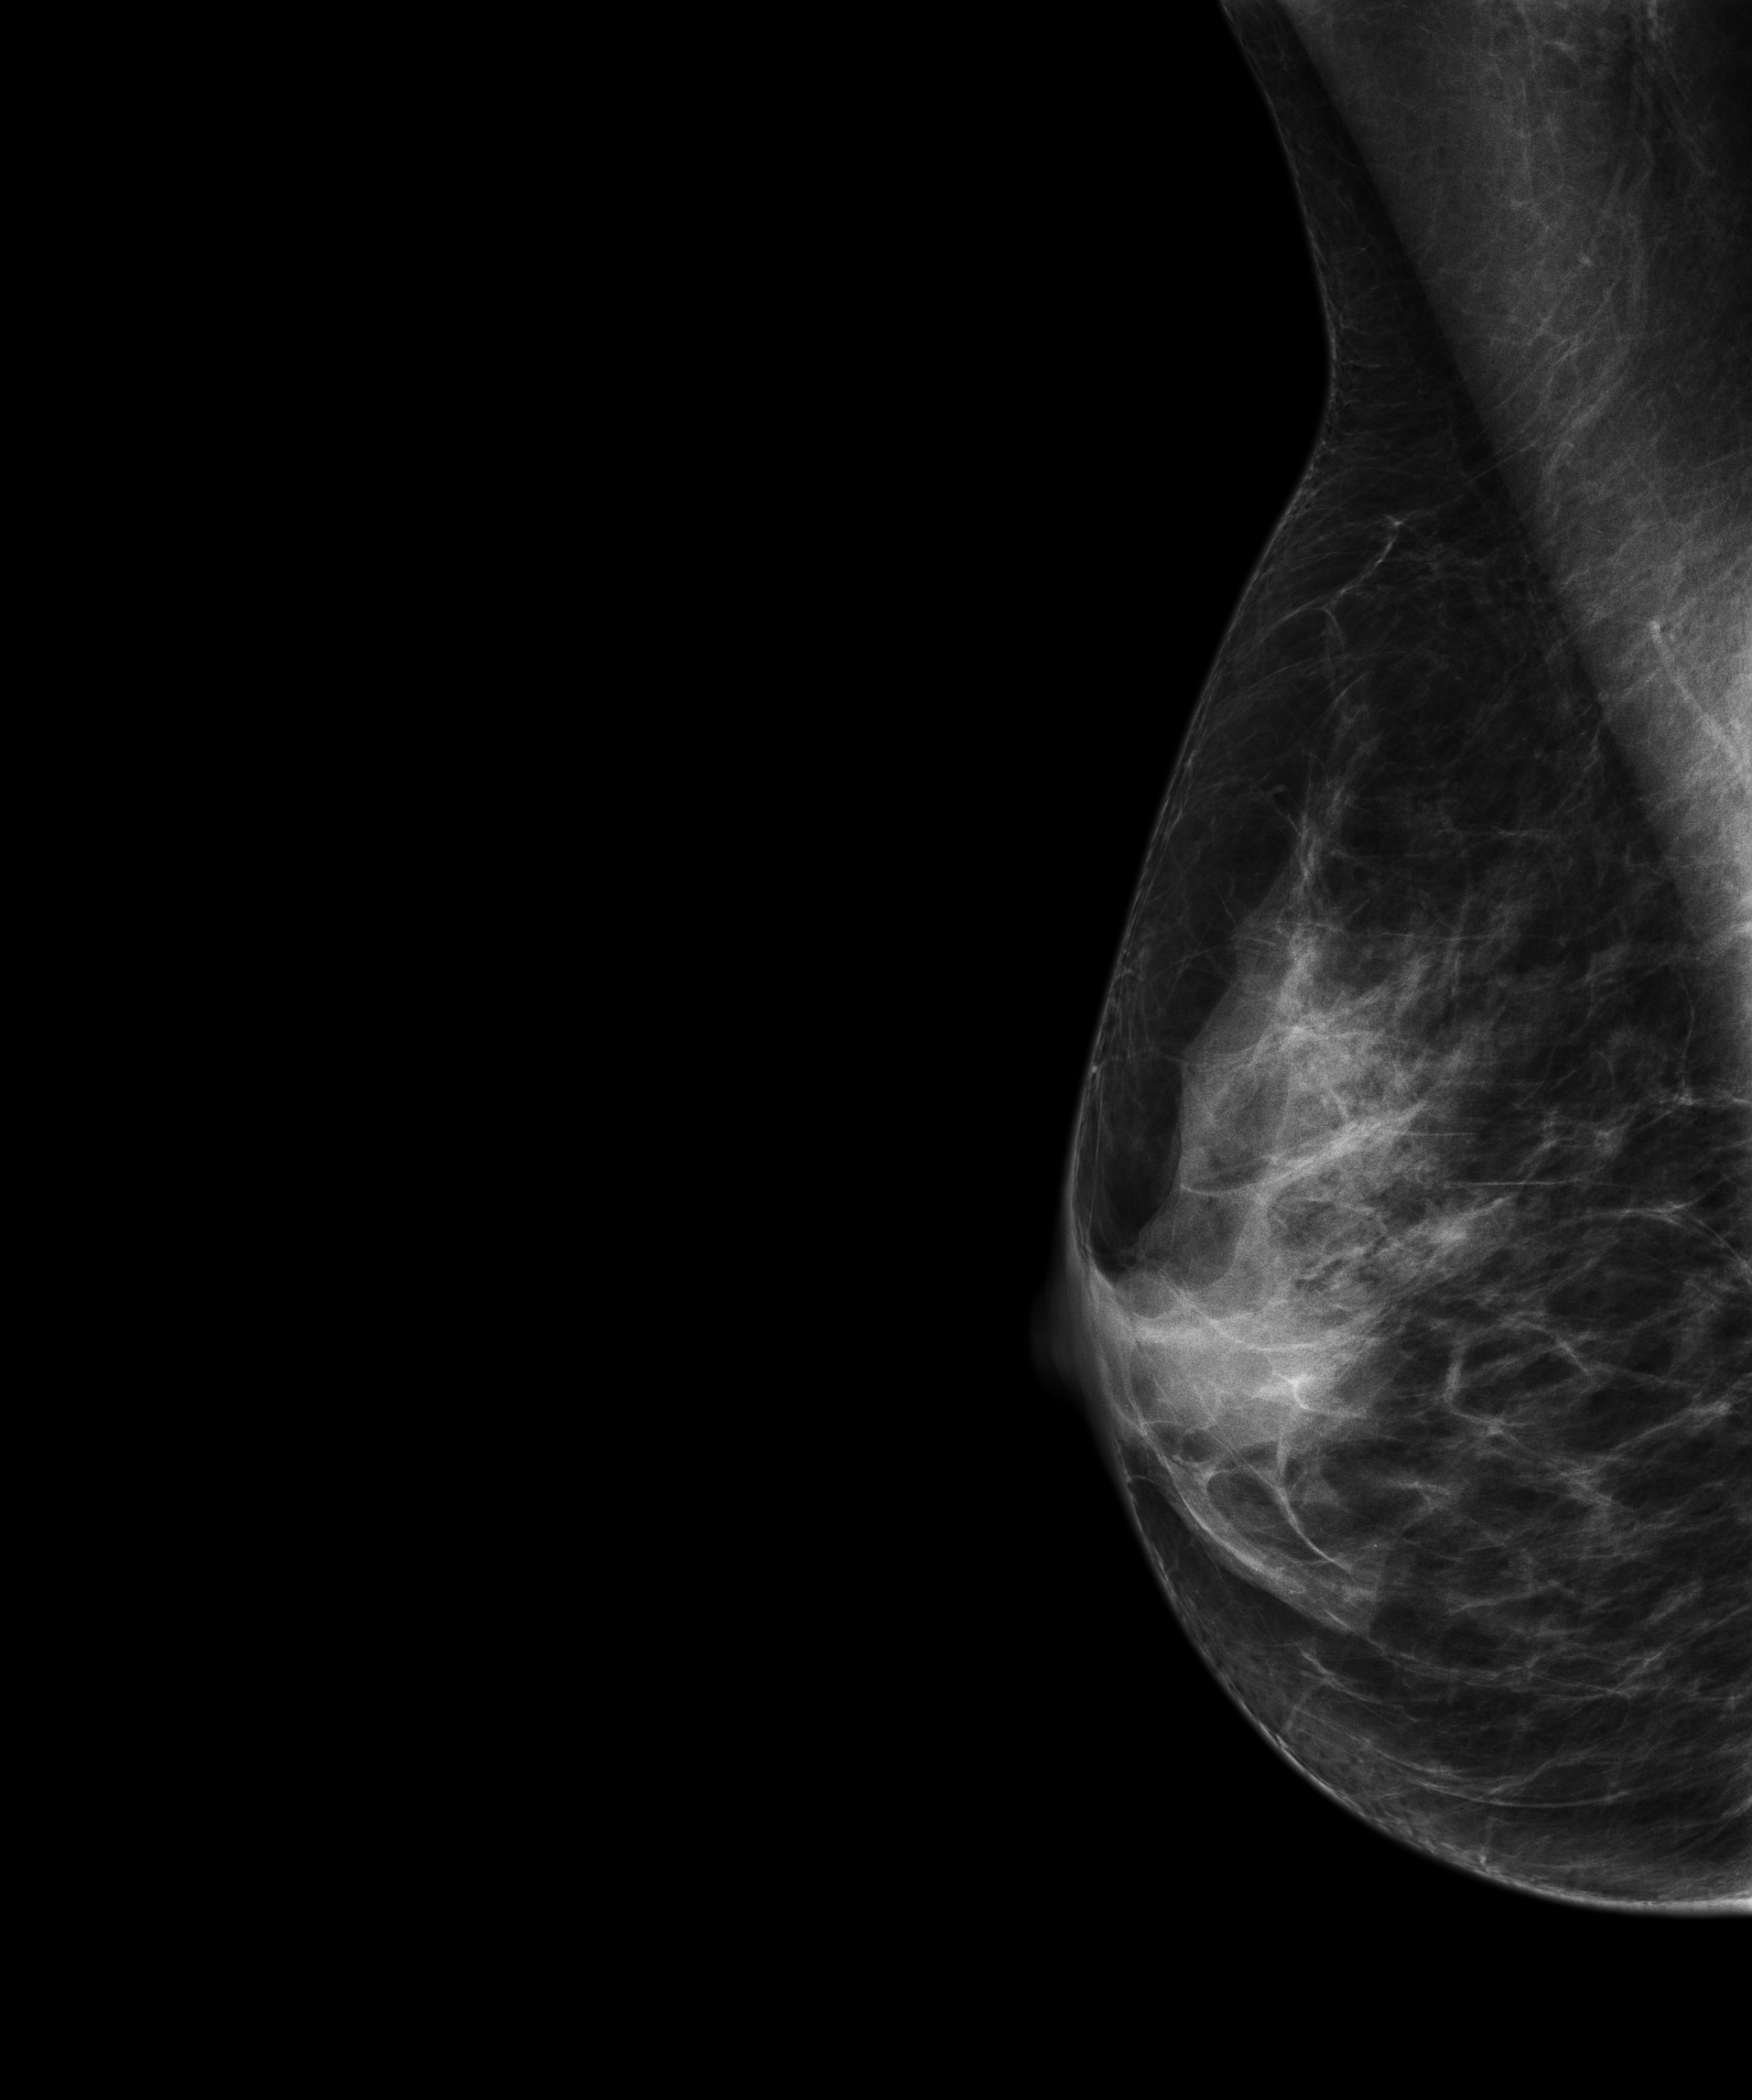
Digital mammogram (FFDM), right breast, mediolateral oblique (MLO) view, annual screening mammography examination, system: Senographe Essential ADS_56.21.3. Patient aged 65 years (female).
BI-RADS breast density category at the screening exam (both breasts, scale 1–4): 3. Final BI-RADS assessment for this screening round (tomosynthesis exam, both breasts): category 1. Recall: no recall after this screen.